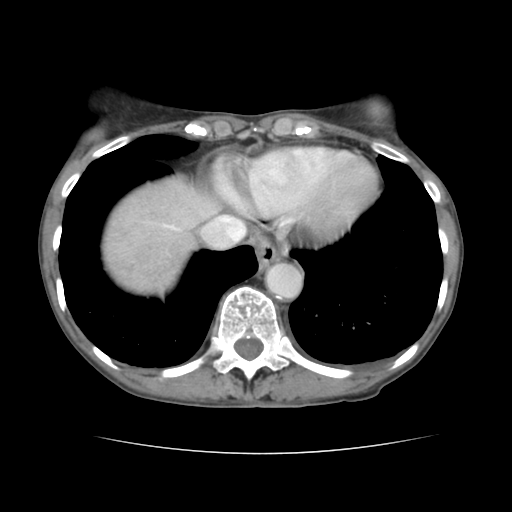
Contrast-enhanced abdominal CT, one axial slice. Position 129 of 136 along the scan axis. 120 kVp. Intravenous contrast given. Soft-tissue window (W 400 / L 40 HU). 512 × 512 image matrix, field of view 319 × 319 mm. Female patient, age 77 years. From the clinical record (not read from this slice): diagnosis: colorectal cancer liver metastases, imaged before liver resection; multiple liver metastases: yes; largest metastasis: 3 cm; chemotherapy before resection: yes.
Annotated regions visible in this slice (expert manual segmentation):
- hepatic veins: bounding box <161,211,245,247> (left, top, right, bottom; pixels)
- liver: <102,179,217,293>
- planned liver remnant (the part of the liver to remain after resection): <208,200,216,210>